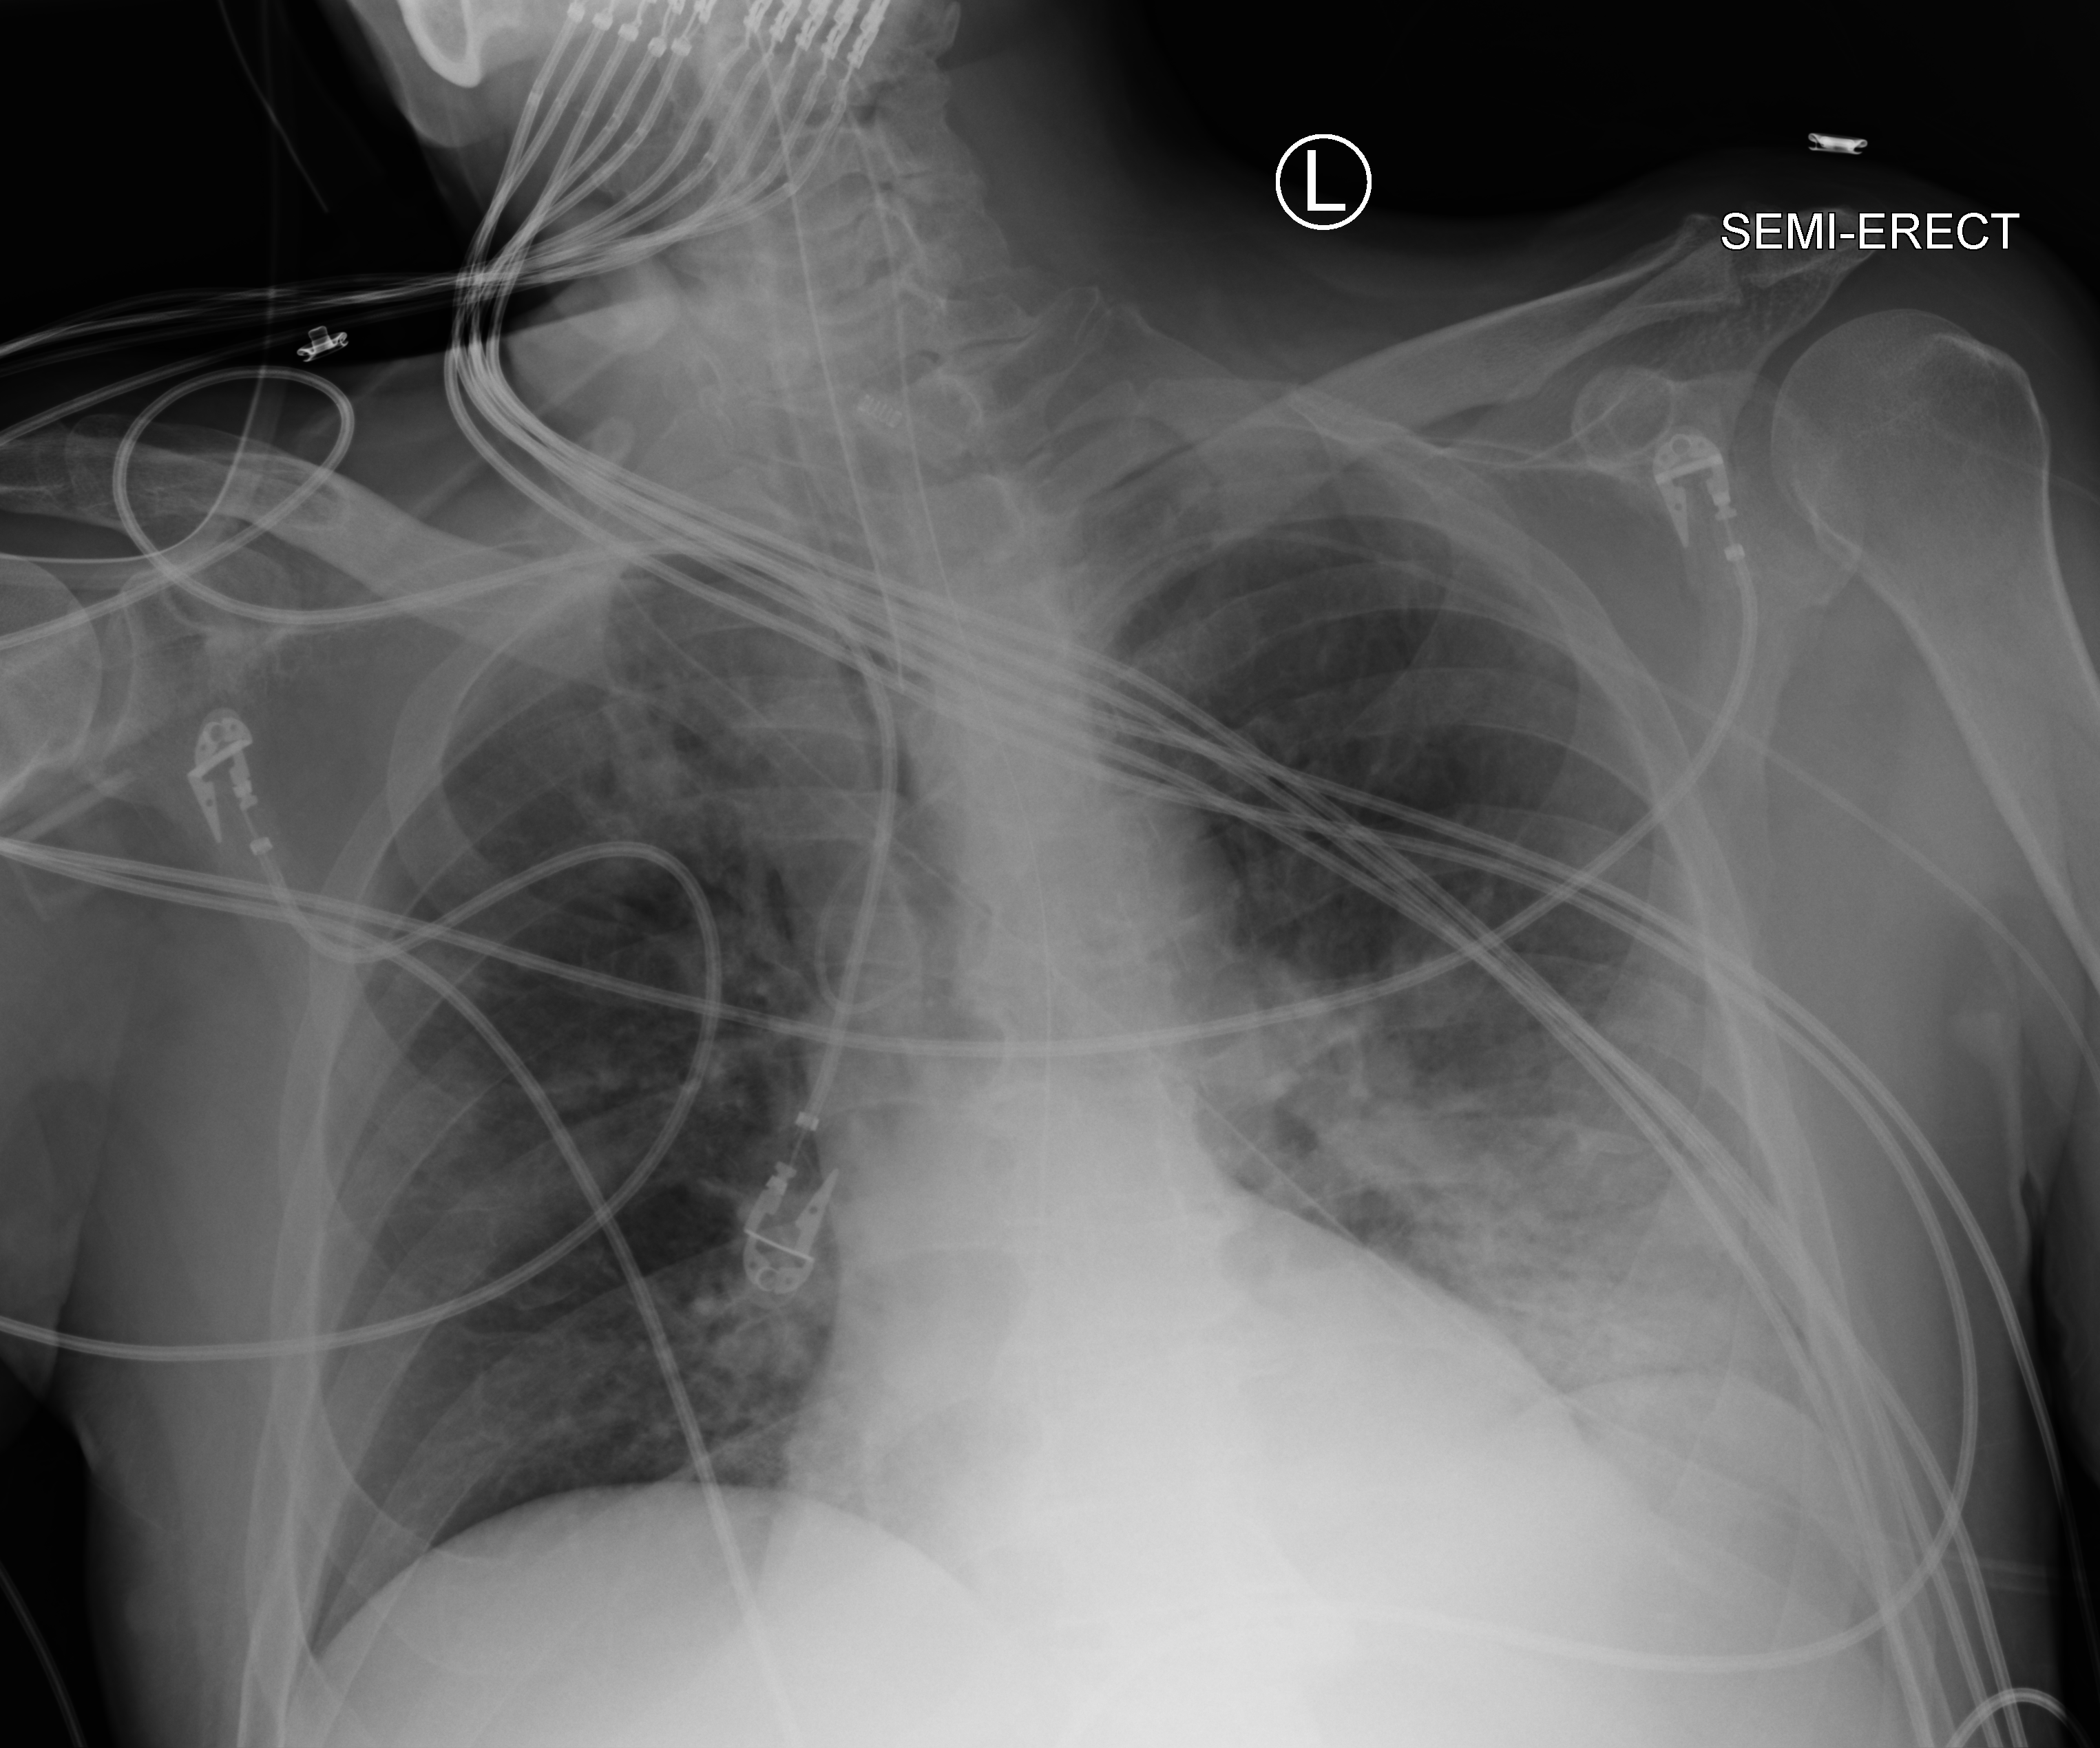
Chest X-ray (portable); anteroposterior (AP) projection. Male patient hospitalised with COVID-19, age 60–74 years.
Admission-level facts for this patient (not findings on this image; timing relative to this image not recorded): length of hospital stay: 35 days; smoking status (admission record): never.